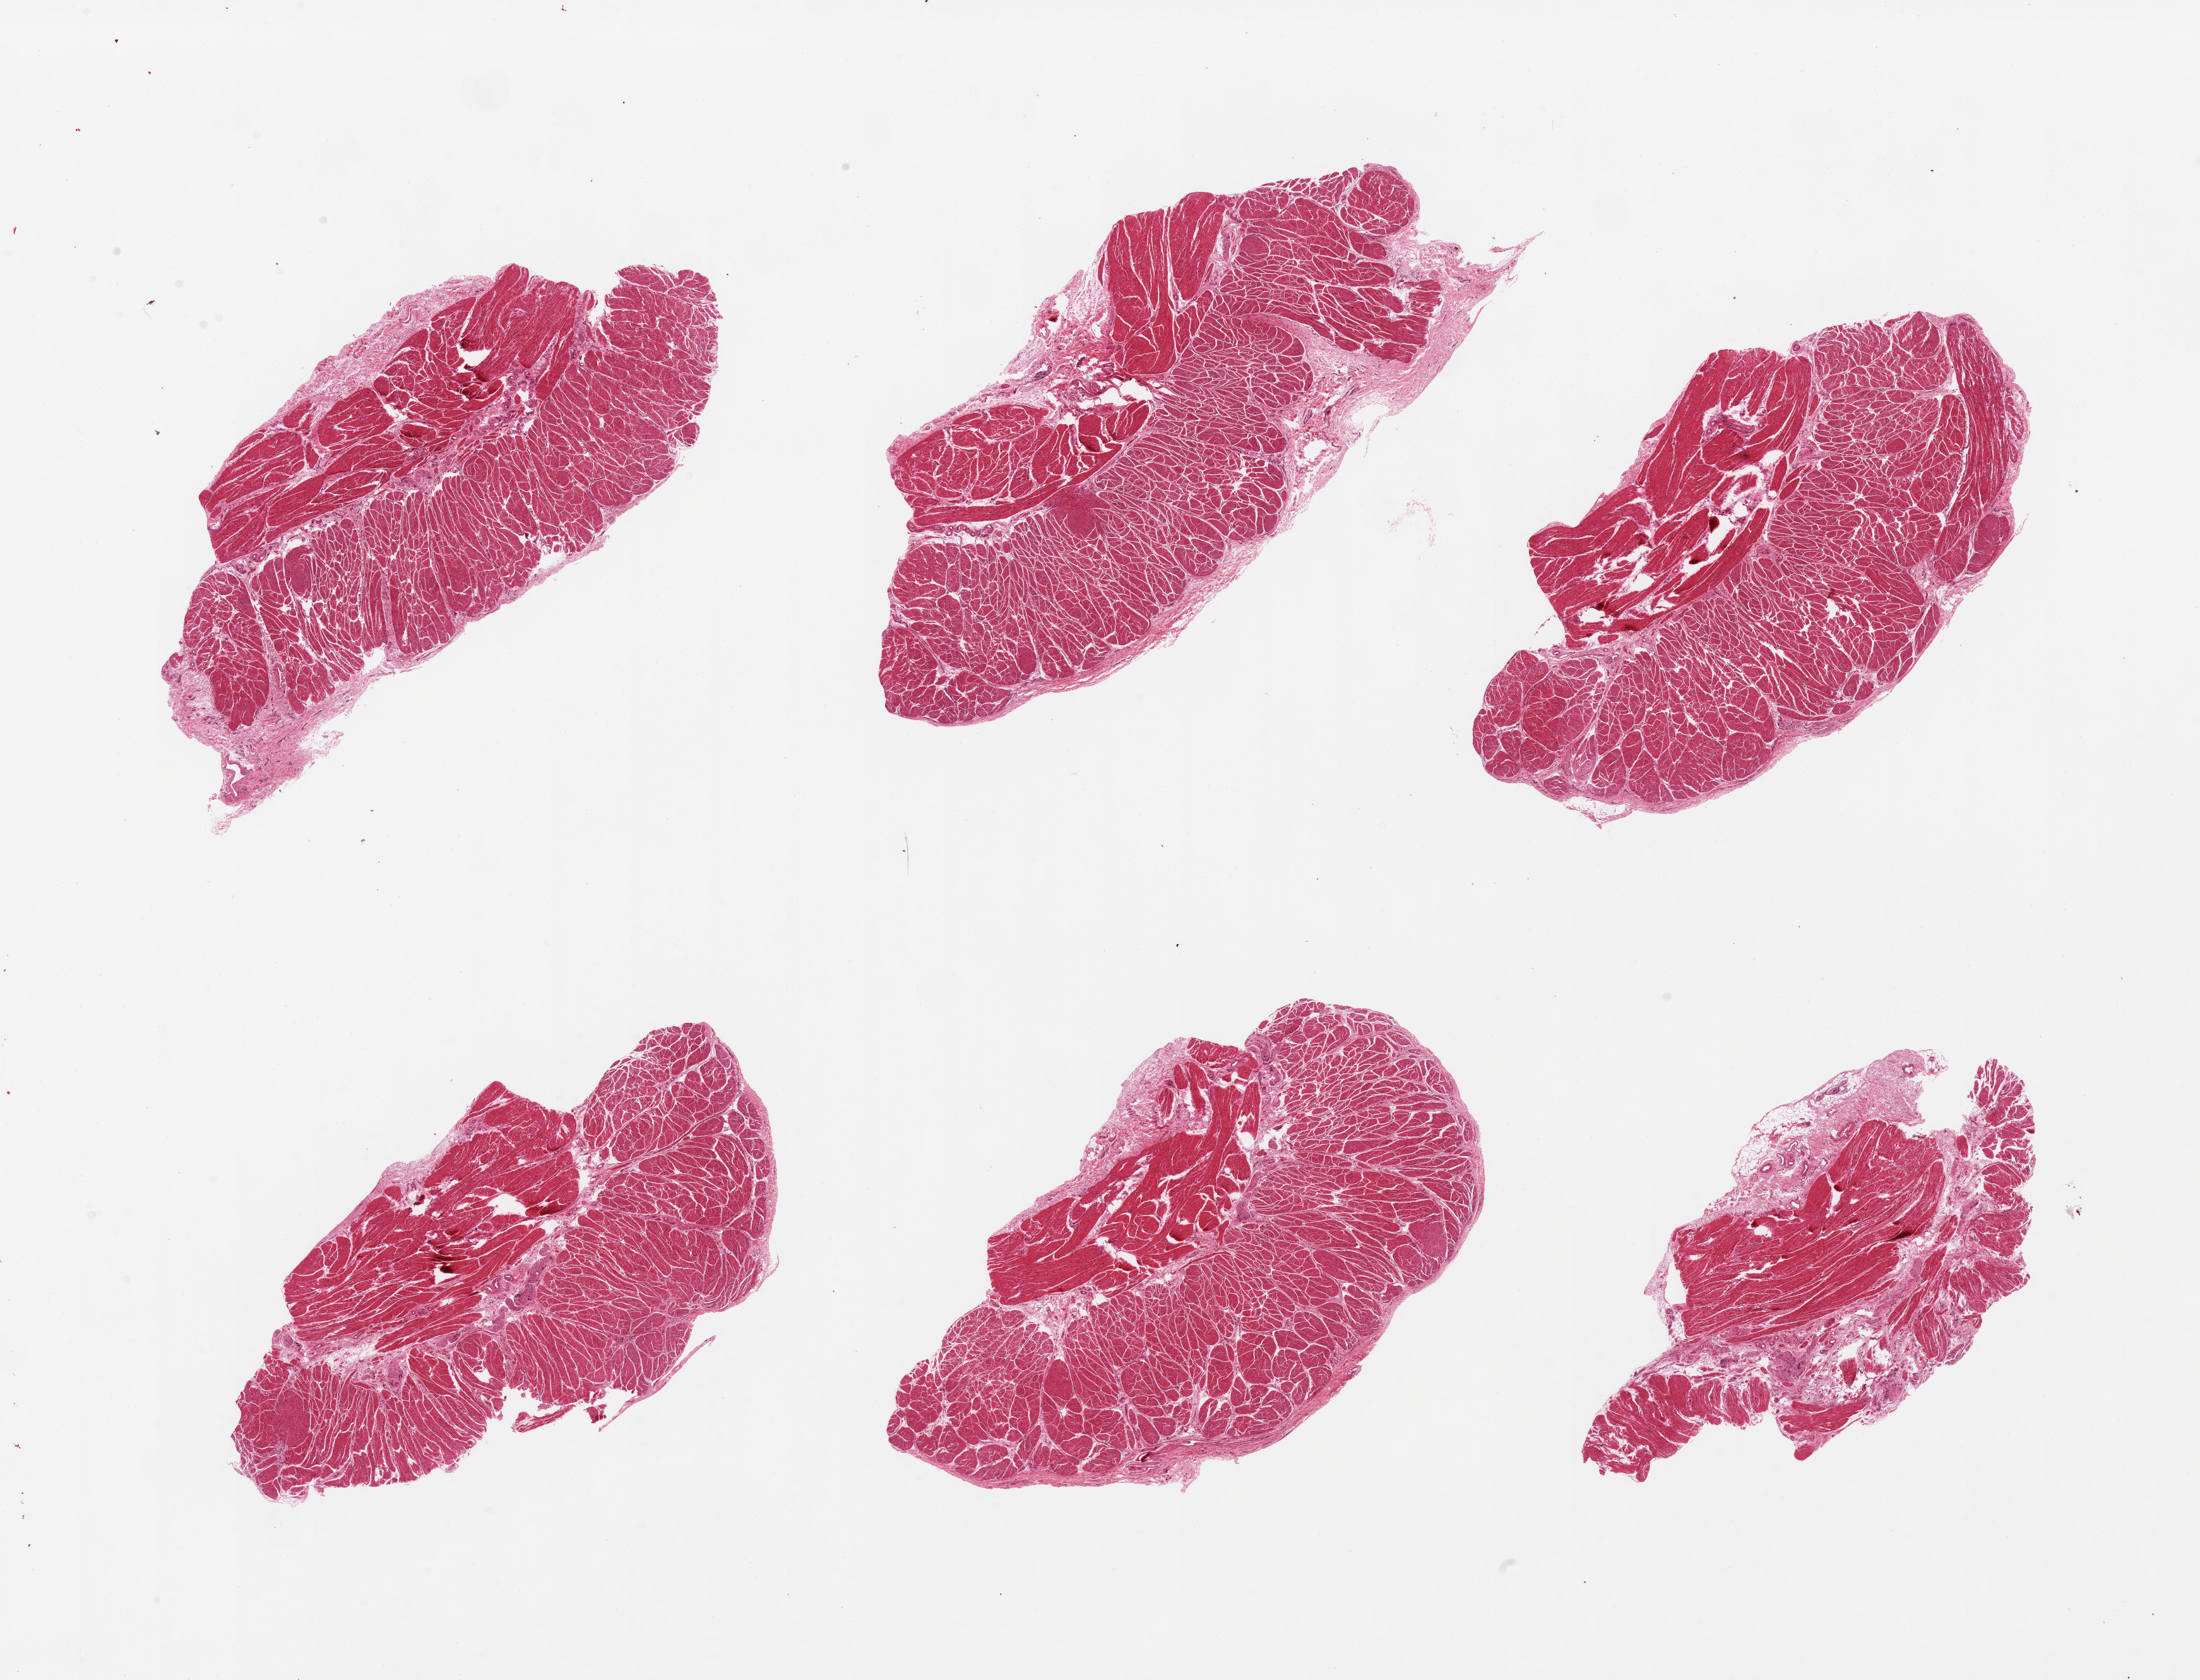
H&E whole-slide image — low-resolution overview of the scanned area, about 27.6 x 21.0 mm; PAXgene-fixed, paraffin-embedded tissue; section of gastroesophageal junction (target tissue); tissue donor sample. Donor sex: male.
Reviewer comment on this tissue sample: 6 pieces, all muscularis.